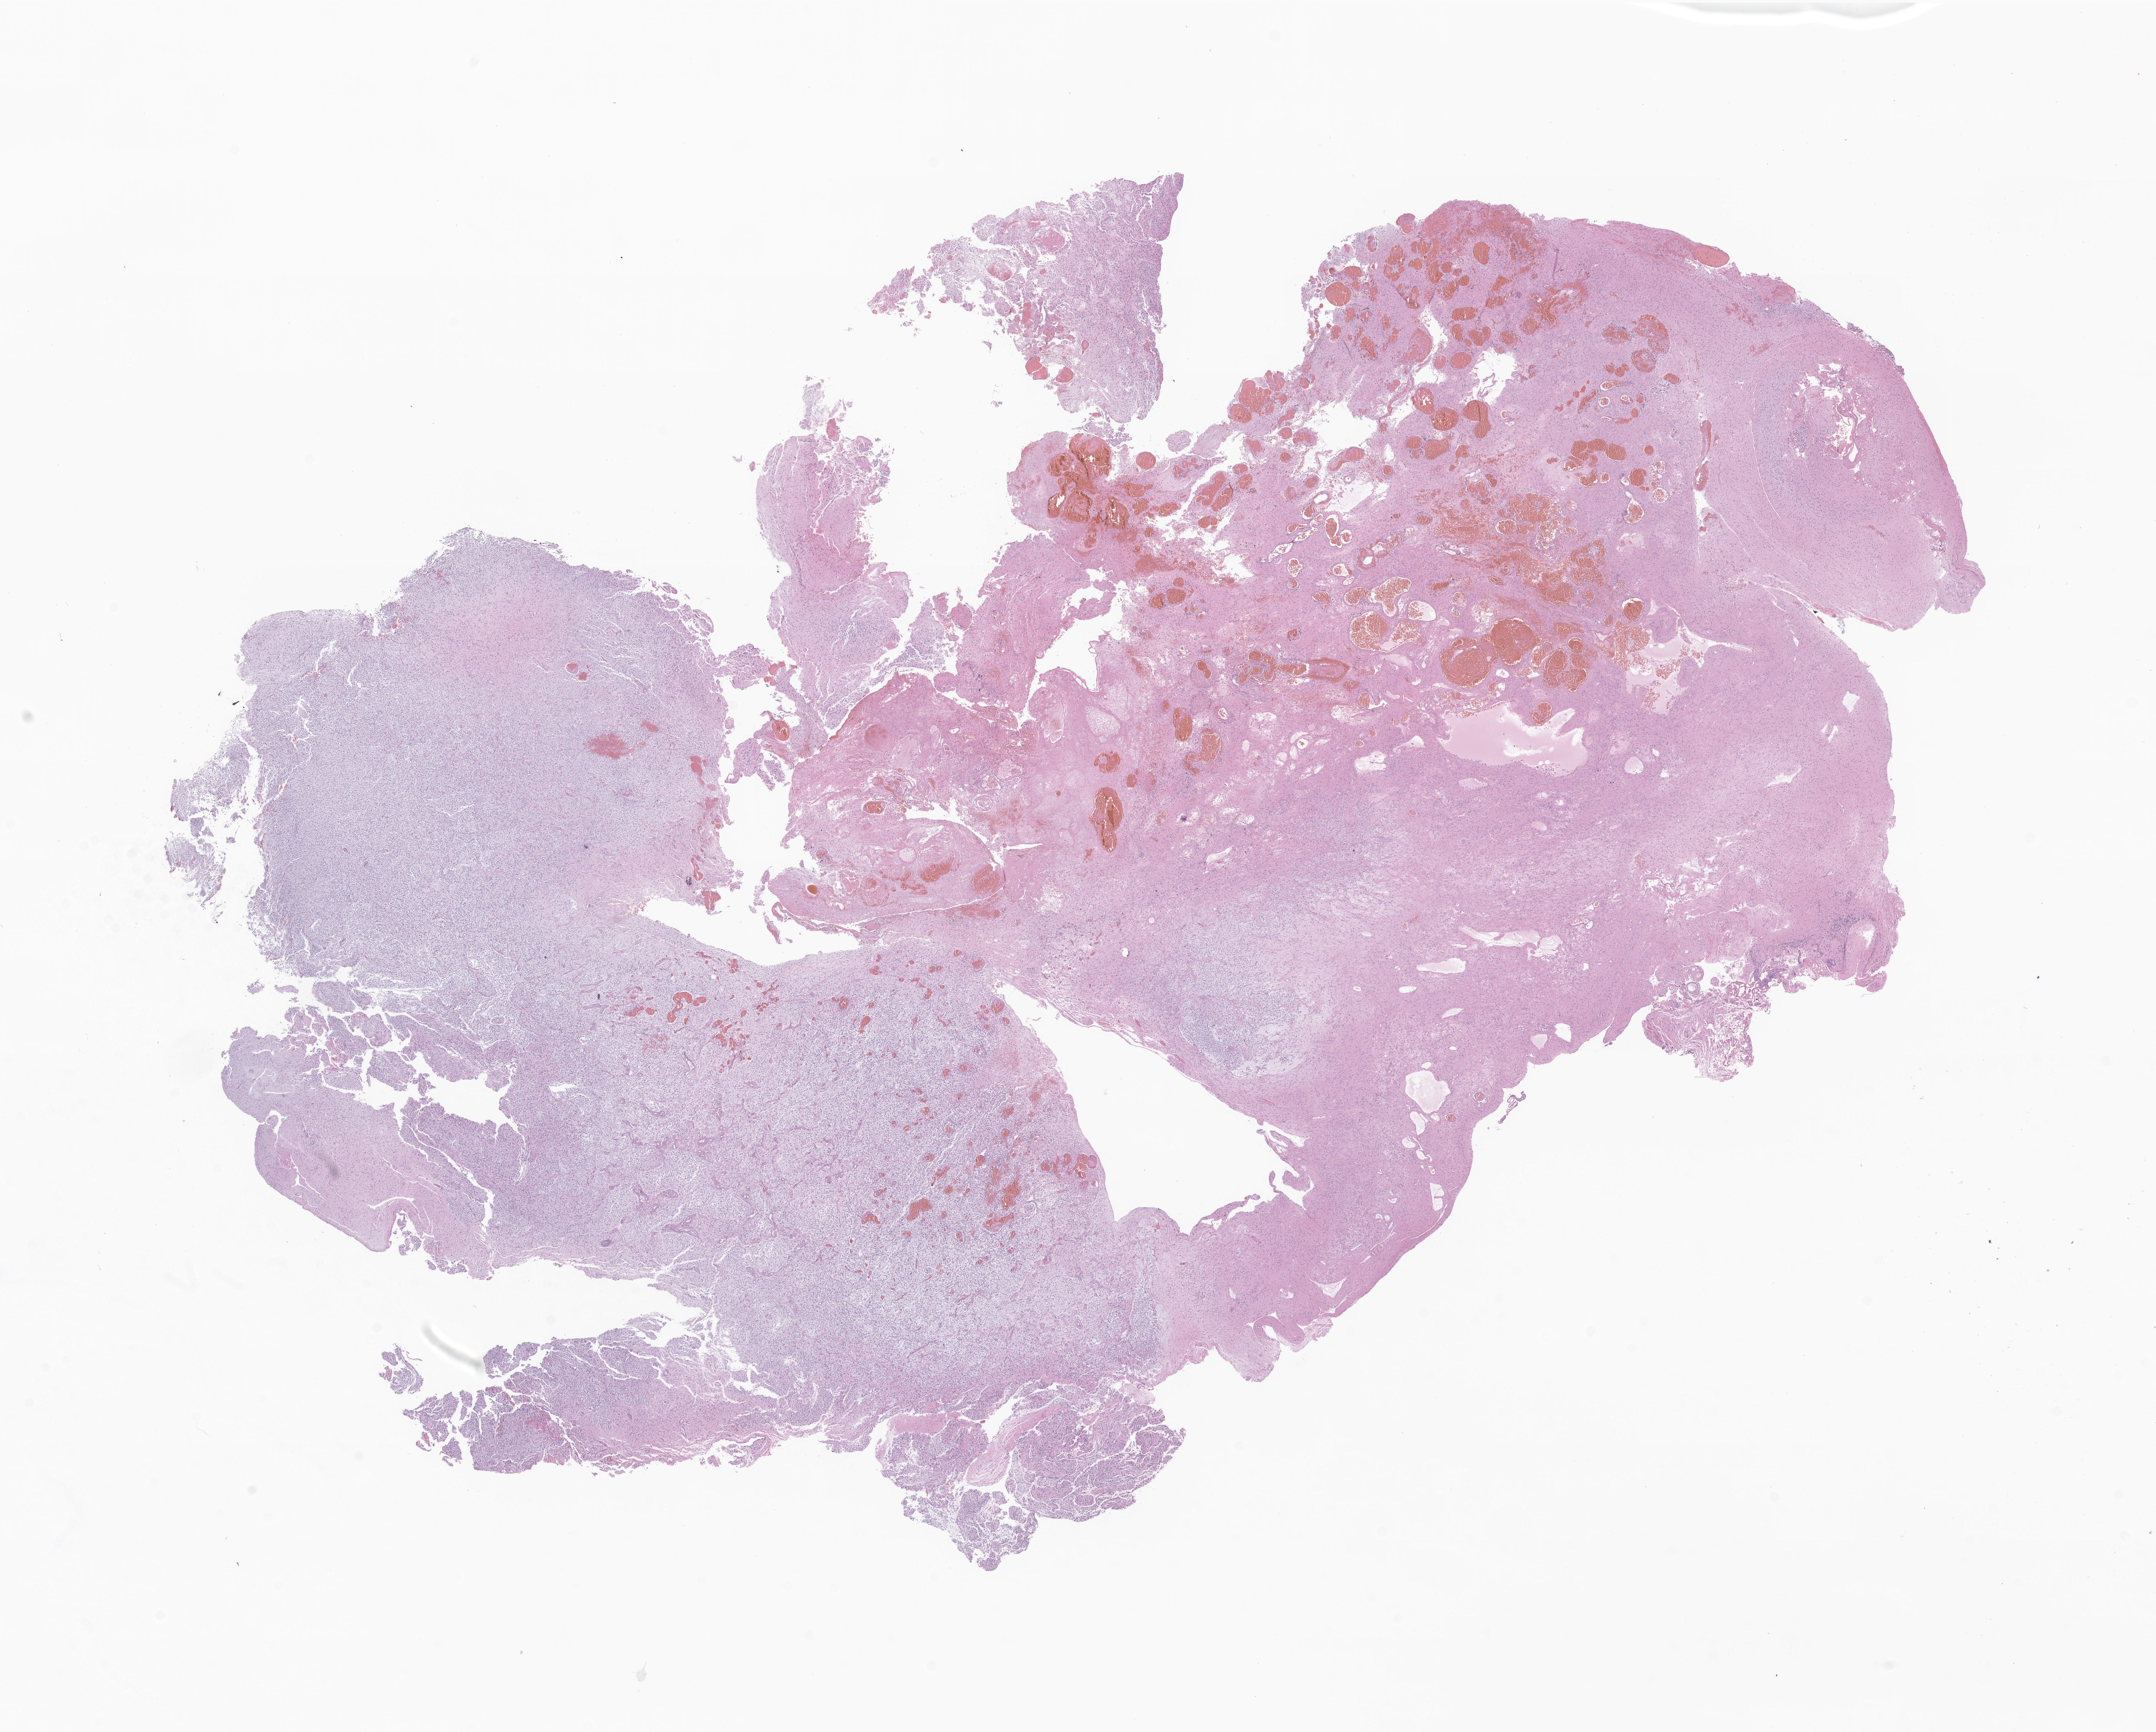
Whole-slide image, H&E stain of tumor tissue from the brain — low-resolution overview of the scanned area, about 23.6 x 19.0 mm, formalin-fixed paraffin-embedded section. Patient male; age 120 months (10 years).
Diagnosis: Oligoastrocytoma, NOS.